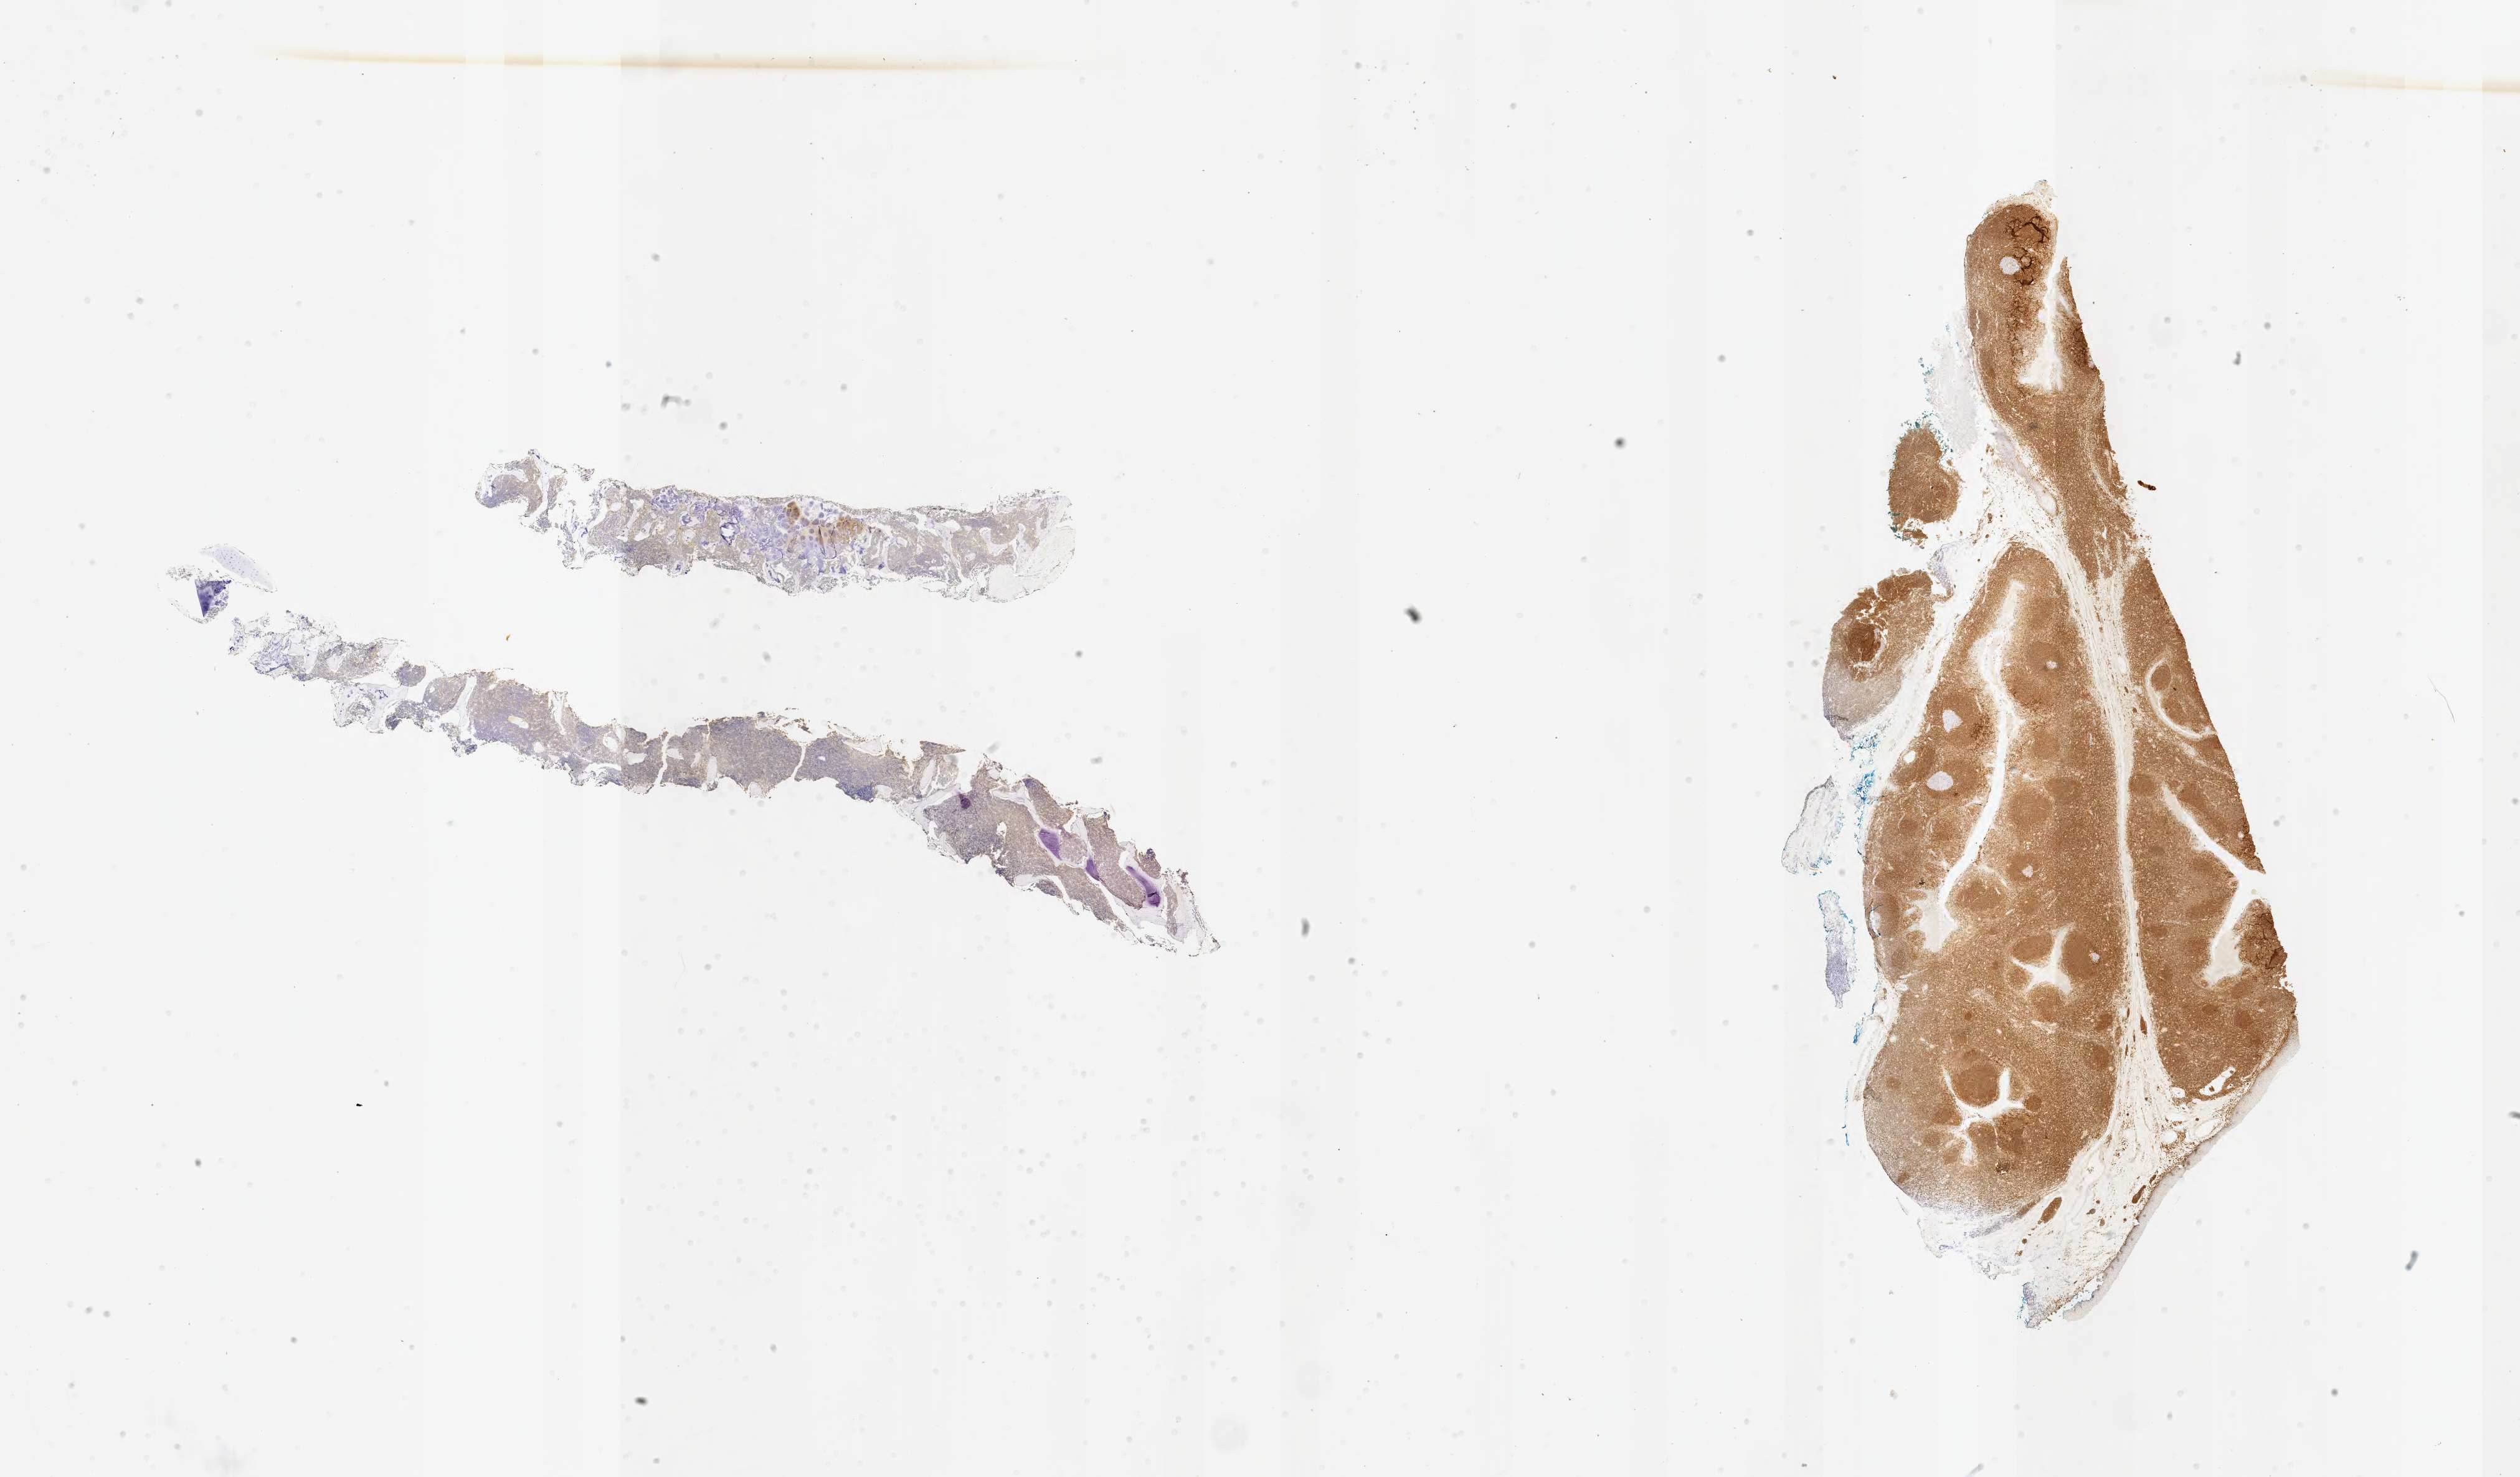
Immunohistochemistry (IHC) whole-slide image stained for BCL2 — shown as a low-resolution overview of the whole scanned area (about 32.7 x 19.2 mm); specimen: tumor tissue; site: bone marrow. Patient: male, 11 years old.
• diagnosis: Burkitt lymphoma, NOS